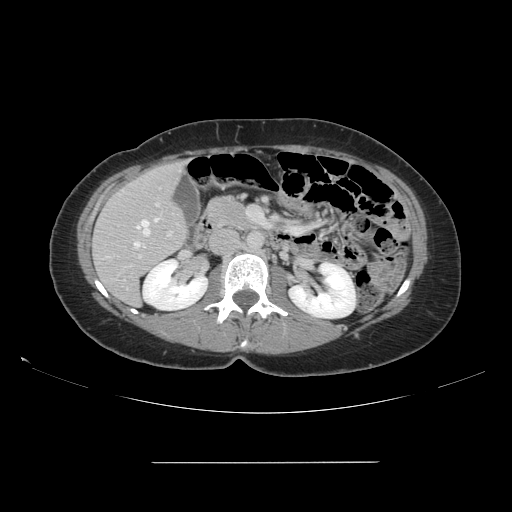
Contrast-enhanced abdominal CT, one axial slice. Slice 71 of 151 in the series (ordered by position). Intravenous contrast given. Soft-tissue window (W 400 / L 40 HU). 2.5 mm slice thickness. 512 × 512 image matrix. Female patient, age 46 years. Case-level facts recorded for this patient, not image findings: diagnosis: colorectal cancer liver metastases, imaged before liver resection; multiple liver metastases: yes; largest metastasis: 3 cm.
Outlined on this slice (expert manual segmentation):
- hepatic veins: box from (x=134, y=218) to (x=159, y=249) px
- liver: (x=93, y=163)–(x=187, y=305)
- planned liver remnant (the part of the liver to remain after resection): (x=93, y=163)–(x=187, y=305)
- portal vein (with intrahepatic branches): (x=130, y=202)–(x=173, y=267)